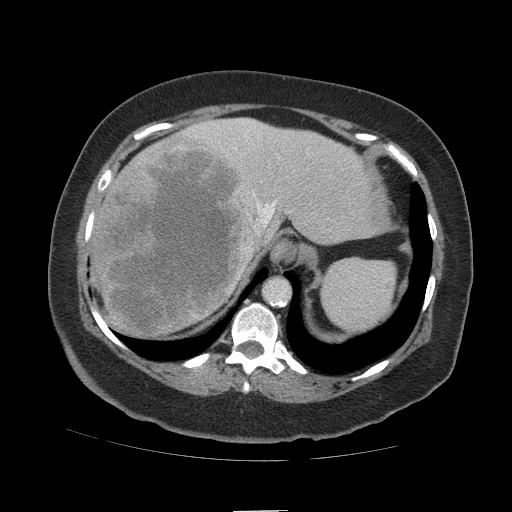
Contrast-enhanced abdominal CT (liver protocol), one axial slice; position 85 of 109 along the scan axis; reconstruction kernel STANDARD; 140 kVp; soft-tissue window (W 400 / L 40 HU); 2.5 mm slice thickness; 512 × 512 image matrix, field of view 420 × 420 mm. Case-level facts recorded for this patient, not image findings: diagnosis: hepatocellular carcinoma (patient treated with transarterial chemoembolisation; whether this scan precedes or follows treatment is not stated here); TNM stage (as recorded): Stage-IVB; Child-Pugh class: A; tumour differentiation: poorly differentiated; tumour nodularity: multinodular.
Outlined on this slice (semi-automatic segmentation, software-assisted and operator-edited):
- abdominal aorta: box from (x=264, y=279) to (x=289, y=301) px
- liver parenchyma outside the tumour (the mass and vessels are separate outlines, so this box may not span the whole liver): (x=92, y=118)–(x=390, y=336)
- mass: (x=93, y=134)–(x=260, y=334)
- liver vessels: (x=193, y=121)–(x=277, y=226)